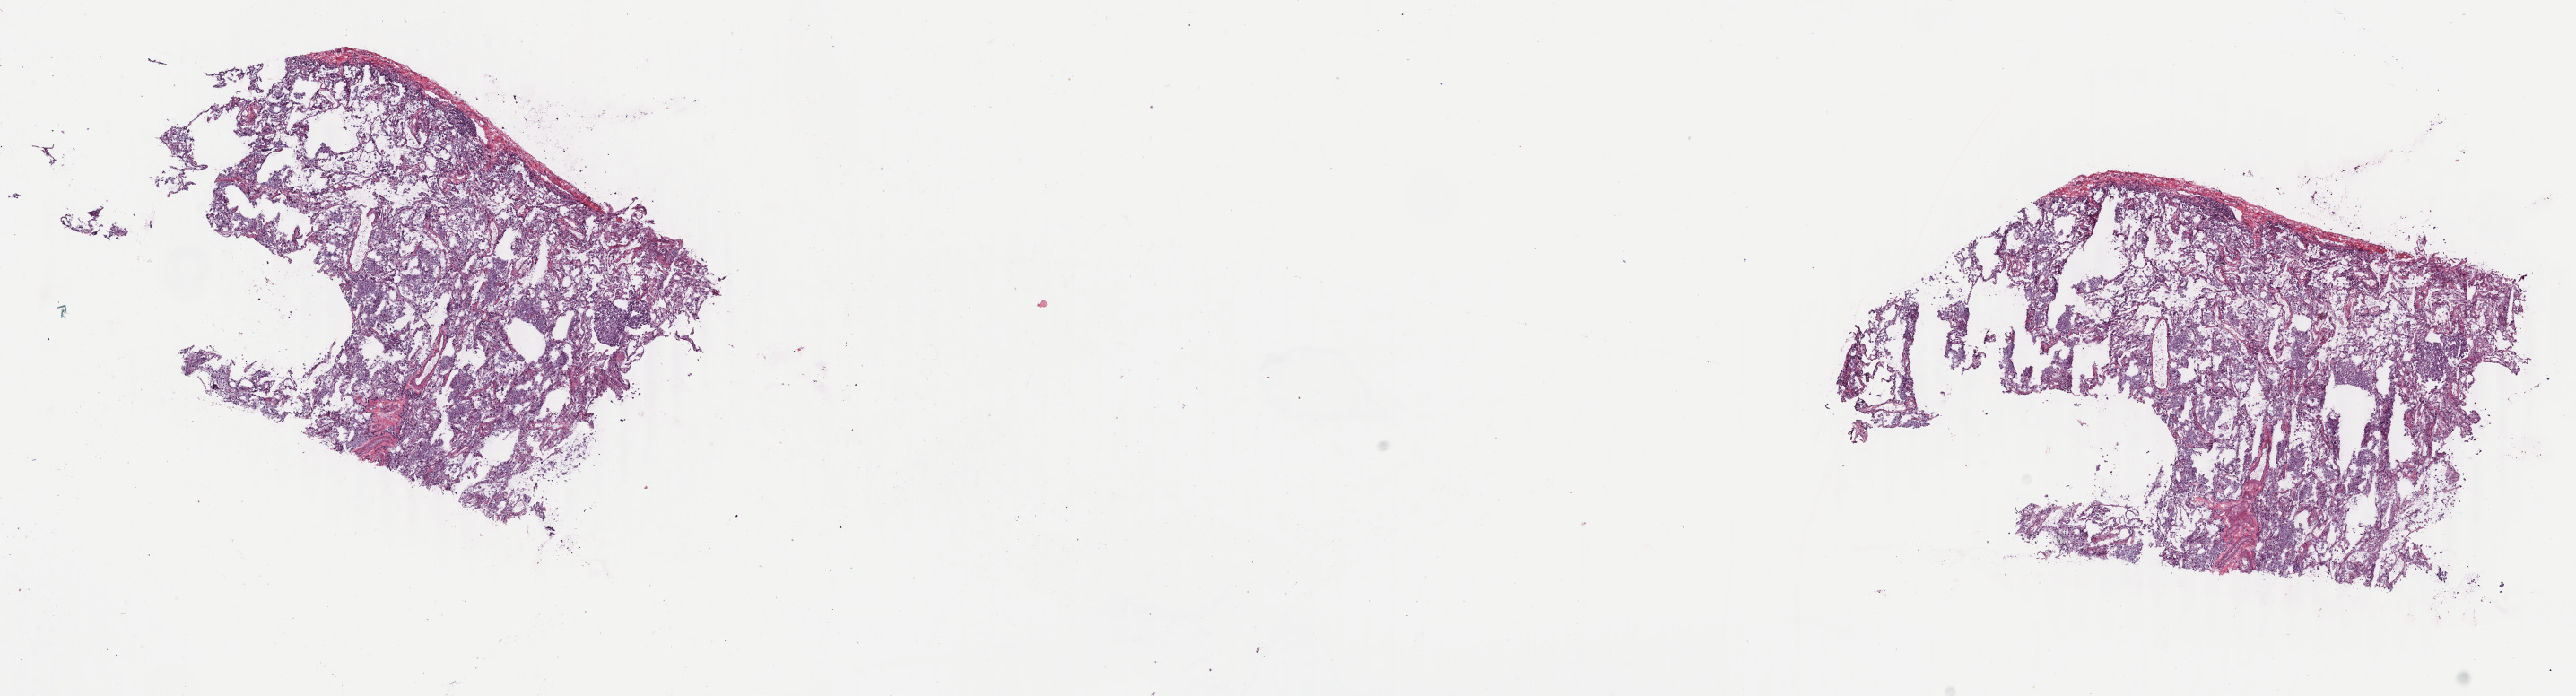
Digitized H&E-stained tissue section (whole slide) — low-resolution overview of the scanned area, about 22.8 x 6.2 mm (acquisition: 40x scan); frozen section; primary tumour sample from the lung. Patient: male, age at initial diagnosis 67 years. Pathologist review of this section (percent, as recorded): tumour cells 100%, tumour nuclei 75%.
Pathologic diagnosis: Adenocarcinoma, NOS (upper lobe, lung).